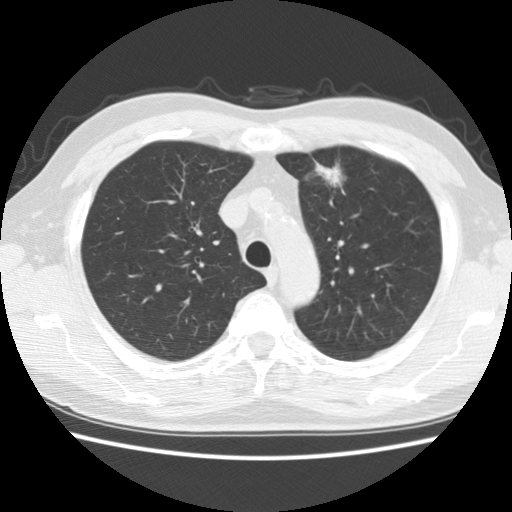
Low-dose screening chest CT, one axial slice. Position 128 of 172 along the scan axis. Reconstruction kernel STANDARD. 120 kVp. Lung window (W 1500 / L -600 HU). 2.5 mm slice thickness. 512 × 512 image matrix, field of view 337 × 337 mm.
Structures marked on this image (manually delineated by an expert):
- lesion 1 (tumor, upper lobe of left lung): bounding box (x1, y1, x2, y2) in pixels: (315, 163, 343, 187)